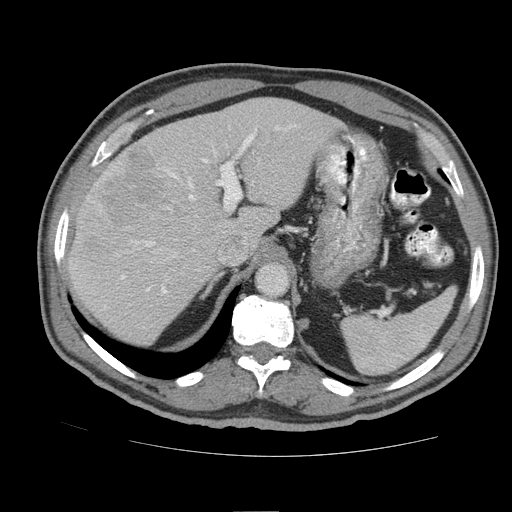
Contrast-enhanced abdominal CT (liver protocol), one axial slice. Position 62 of 105 along the scan axis. Reconstruction kernel STANDARD. Soft-tissue window (W 400 / L 40 HU). 512 × 512 image matrix, field of view 380 × 380 mm. Case-level facts recorded for this patient, not image findings: diagnosis: hepatocellular carcinoma (patient treated with transarterial chemoembolisation; whether this scan precedes or follows treatment is not stated here); TNM stage (as recorded): Stage-IIIB; Child-Pugh class: A; tumour nodularity: multinodular.
Structures marked on this image (semi-automatically segmented with operator editing):
- liver parenchyma outside the tumour (the mass and vessels are separate outlines, so this box may not span the whole liver): bounding box <68,98,340,344> (left, top, right, bottom; pixels)
- mass: <84,141,180,254>
- liver vessels: <93,126,280,293>